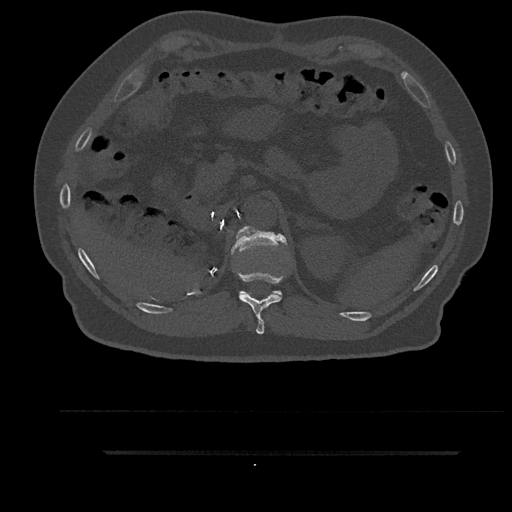
CT including the spine, one axial slice; position 280 of 797 along the scan axis; reconstruction kernel Br40s/3; 120 kVp; bone window (W 1800 / L 400 HU); 512 × 512 image matrix, field of view 432 × 432 mm. Male patient, age 63 years. Case-level facts recorded for this patient, not image findings: primary cancer: renal; vertebrae with lytic lesions (as recorded): T8.
Structures marked on this image (semi-automatic segmentation, software-assisted and operator-edited):
- T11 vertebra: bounding box <237,232,282,334> (left, top, right, bottom; pixels)
- T12 vertebra: <231,226,287,295>